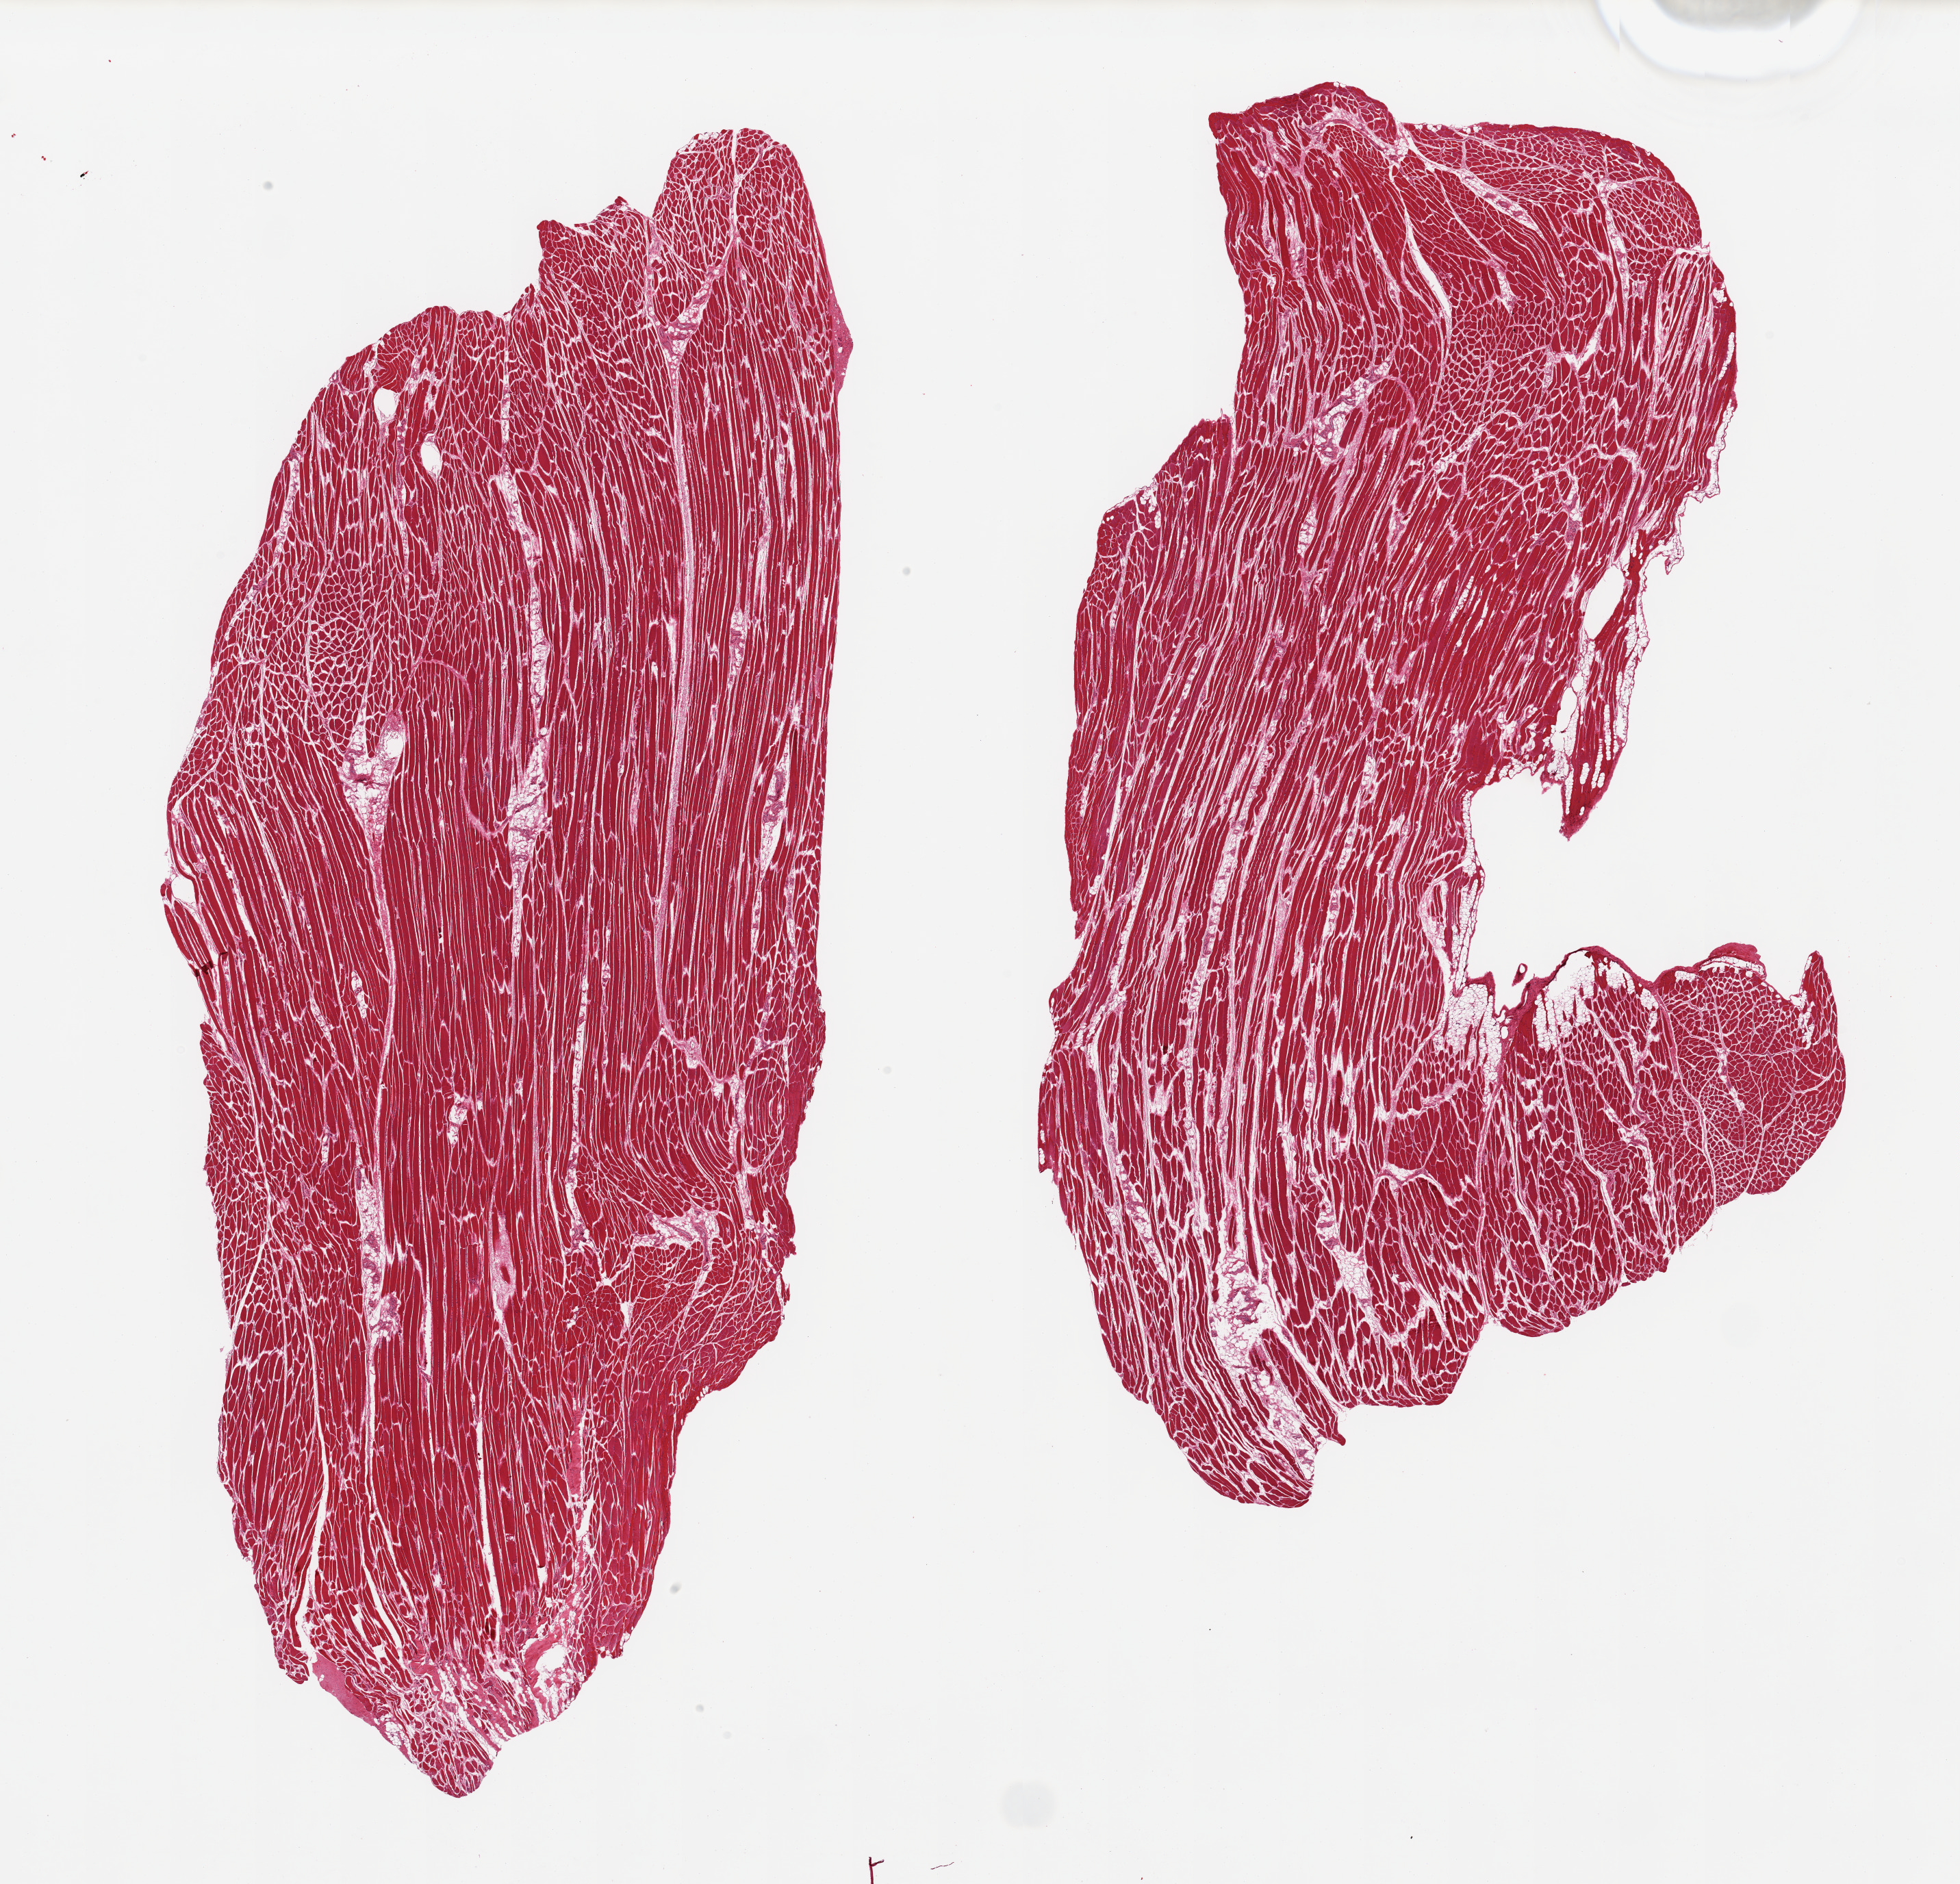
Haematoxylin and eosin whole-slide image — whole scanned area (about 22.6 x 21.8 mm, from a 20x scan) shown as a low-resolution overview. PAXgene-fixed, paraffin-embedded tissue. Target tissue: skeletal muscle. Donor tissue sample. Female donor.
Pathologist's review note for this sample: 6 pieces, some fibers appear mildly atrophied. Minimal interstitial fat, ~5-10%.